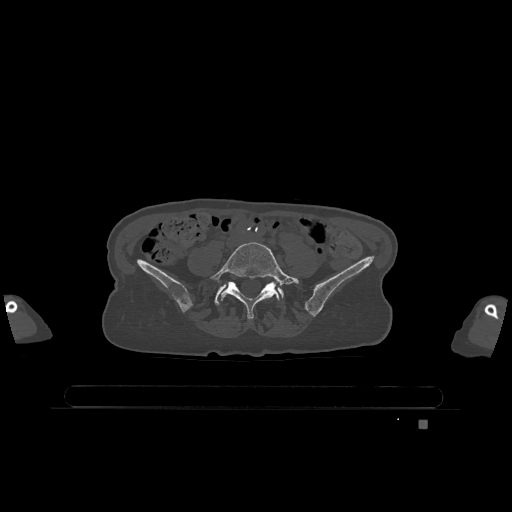
CT including the spine, one axial slice; slice 240 of 1317 in the series (ordered by position); bone window (W 1800 / L 400 HU); 0.5 mm slice thickness; 512 × 512 image matrix, field of view 500 × 500 mm. Patient: female, 74 years. From the clinical record (not read from this slice): primary cancer: lung; vertebrae with lytic lesions (as recorded): T1, T4, T5, T6, L4, L5.
Outlined on this slice (semi-automatically segmented with operator editing):
- L5 vertebra: bounding box <210,242,299,319> (left, top, right, bottom; pixels)